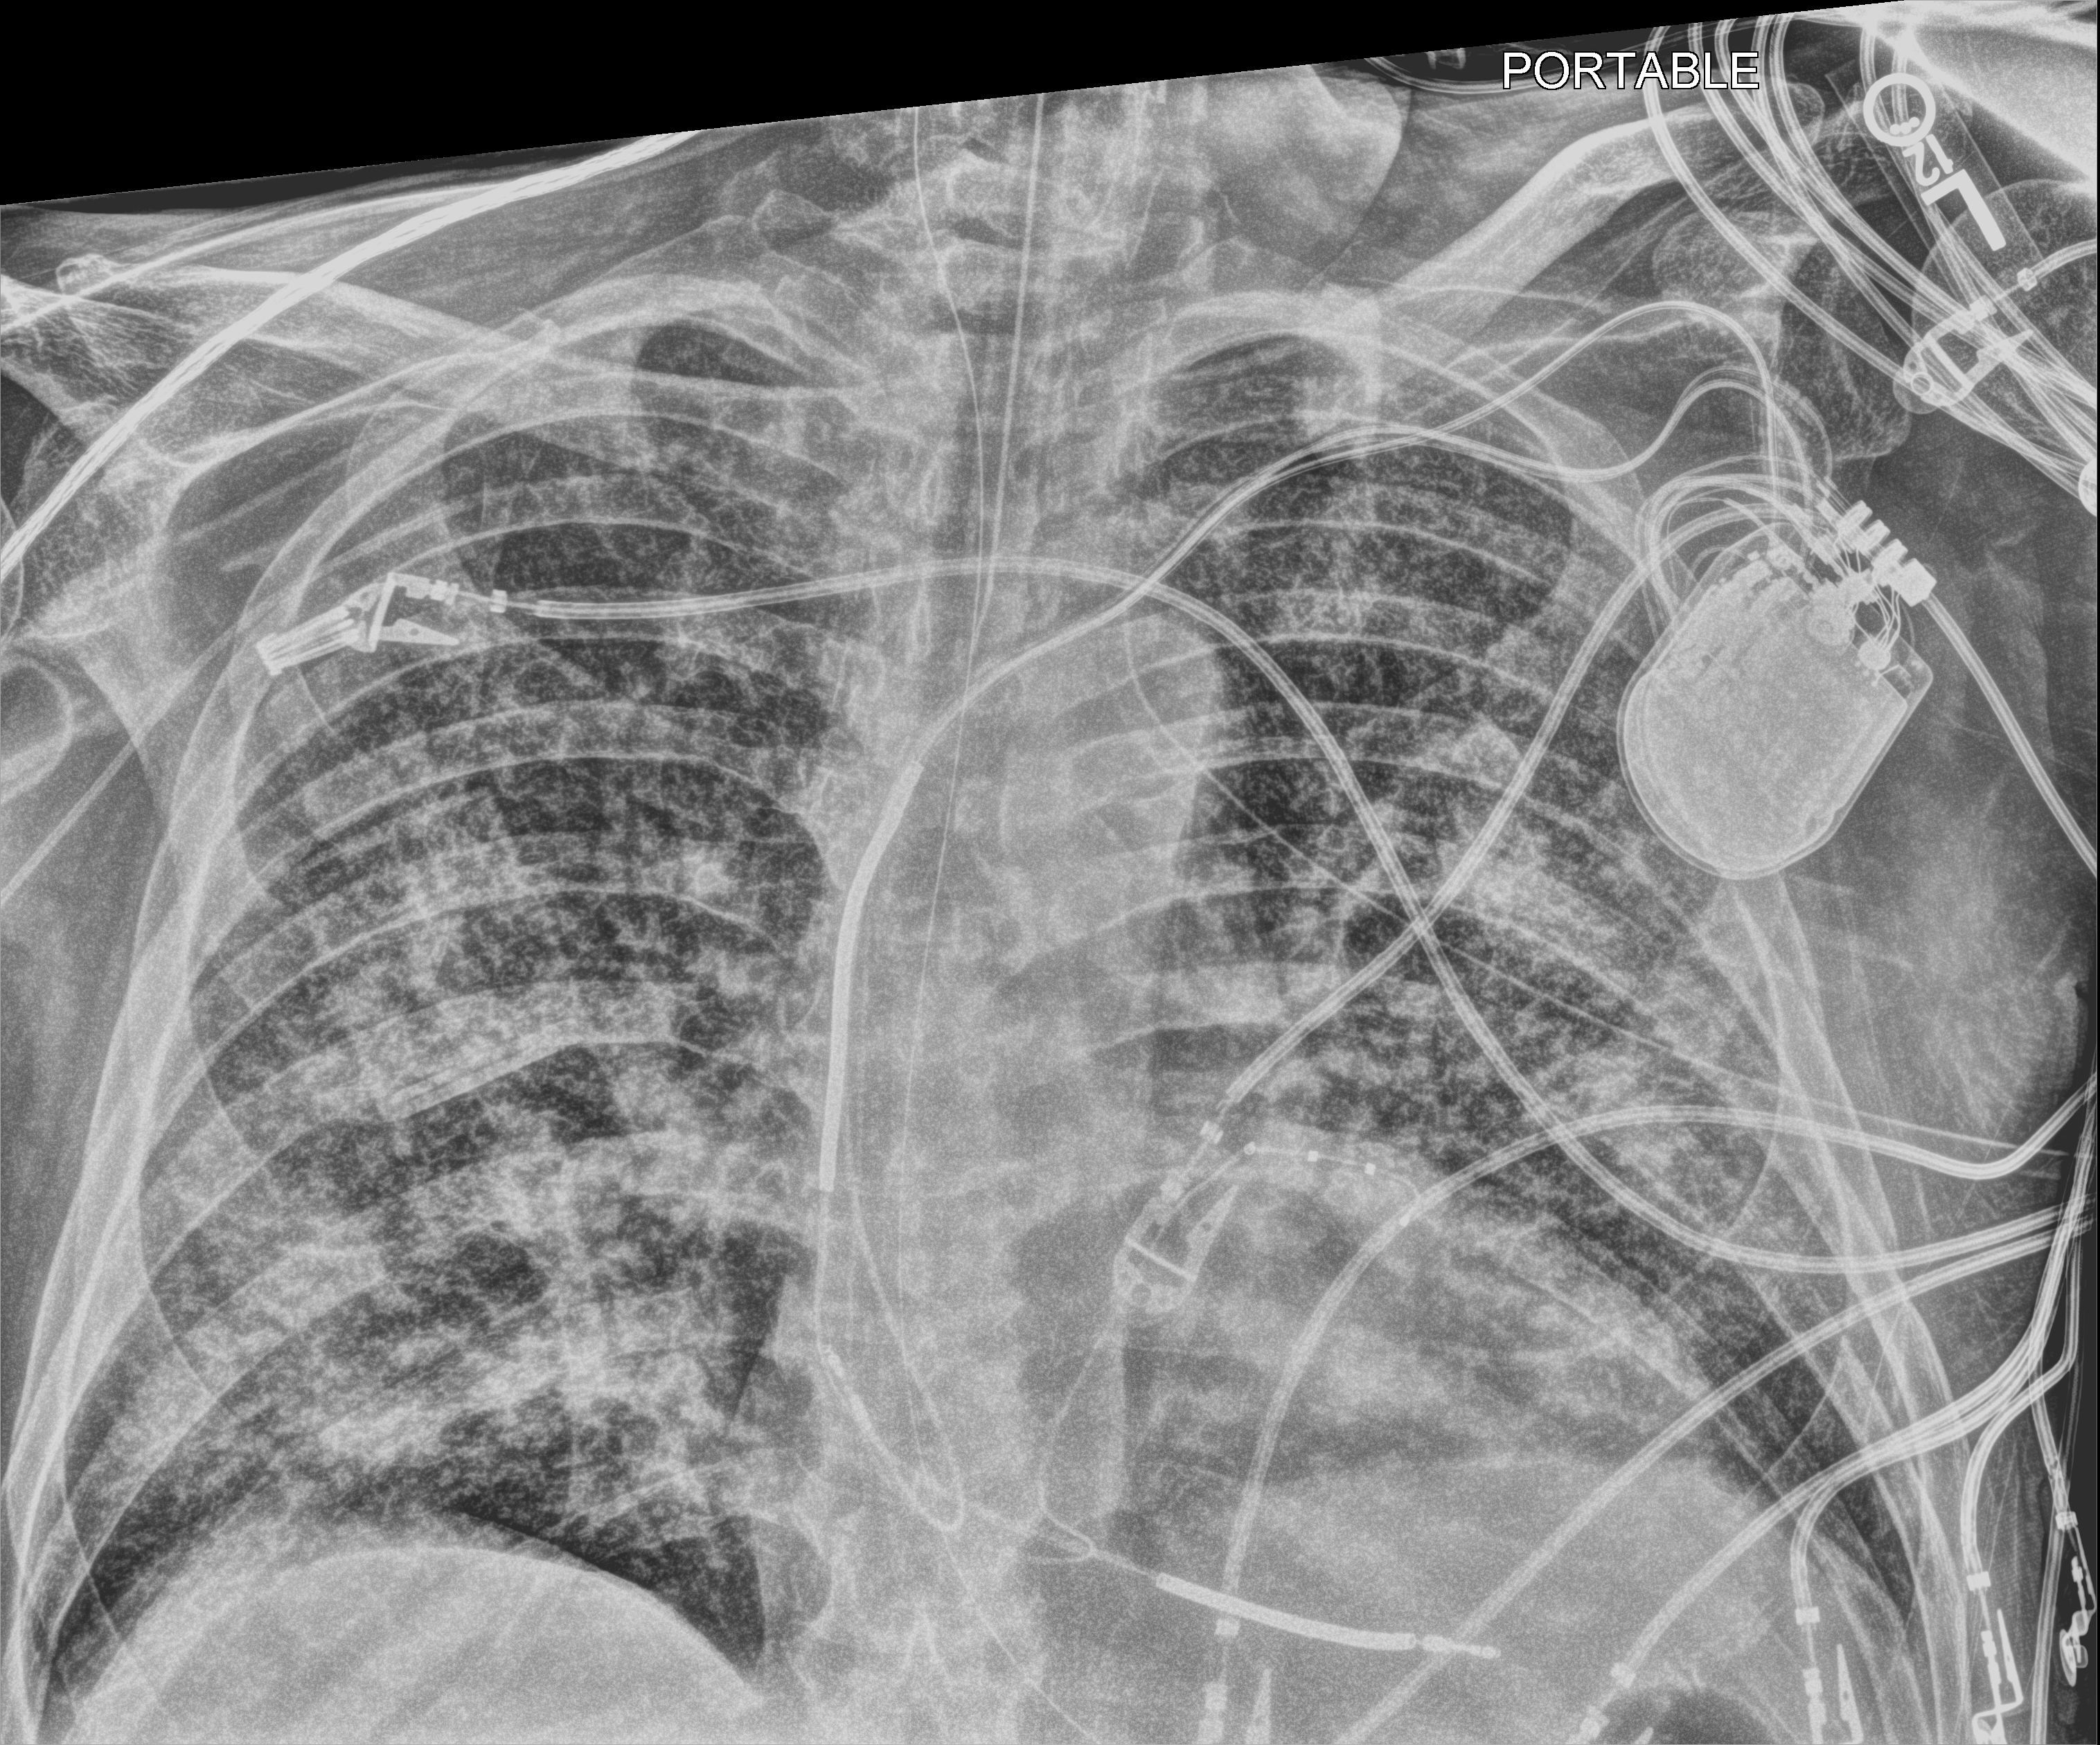
Portable chest radiograph, anteroposterior (AP) projection. Patient hospitalised with COVID-19; male, aged 60–74 years.
Admission-level facts for this patient (not findings on this image; timing relative to this image not recorded):
- length of hospital stay: 36 days